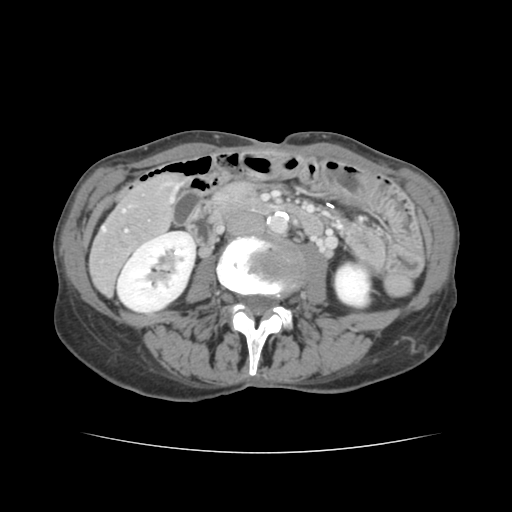
Contrast-enhanced abdominal CT, one axial slice; slice 38 of 136 in the series (ordered by position); intravenous contrast given; soft-tissue window (W 400 / L 40 HU); 2.5 mm slice thickness; 512 × 512 image matrix. Female patient, age 77 years. From the clinical record (not read from this slice): diagnosis: colorectal cancer liver metastases, imaged before liver resection; multiple liver metastases: yes; largest metastasis: 3 cm; chemotherapy before resection: yes.
Structures marked on this image (expert manual segmentation):
- hepatic veins: bounding box <103,186,177,231> (left, top, right, bottom; pixels)
- liver: <90,175,180,292>